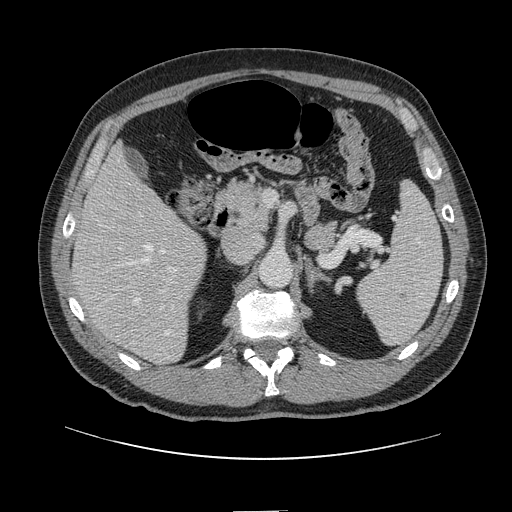
Contrast-enhanced abdominal CT, one axial slice. Position 68 of 161 along the scan axis. 120 kVp. Intravenous contrast given. Soft-tissue window (W 400 / L 40 HU). 2.5 mm slice thickness. 512 × 512 image matrix, field of view 412 × 412 mm. Male patient, age 66 years. Case-level facts recorded for this patient, not image findings: diagnosis: colorectal cancer liver metastases, imaged before liver resection; multiple liver metastases: no.
Outlined on this slice (outlined manually by an expert reader):
- hepatic veins: bounding box [x1, y1, x2, y2] px = [118, 160, 169, 335]
- liver: [75, 149, 205, 363]
- planned liver remnant (the part of the liver to remain after resection): [75, 149, 182, 289]
- portal vein (with intrahepatic branches): [119, 212, 179, 312]